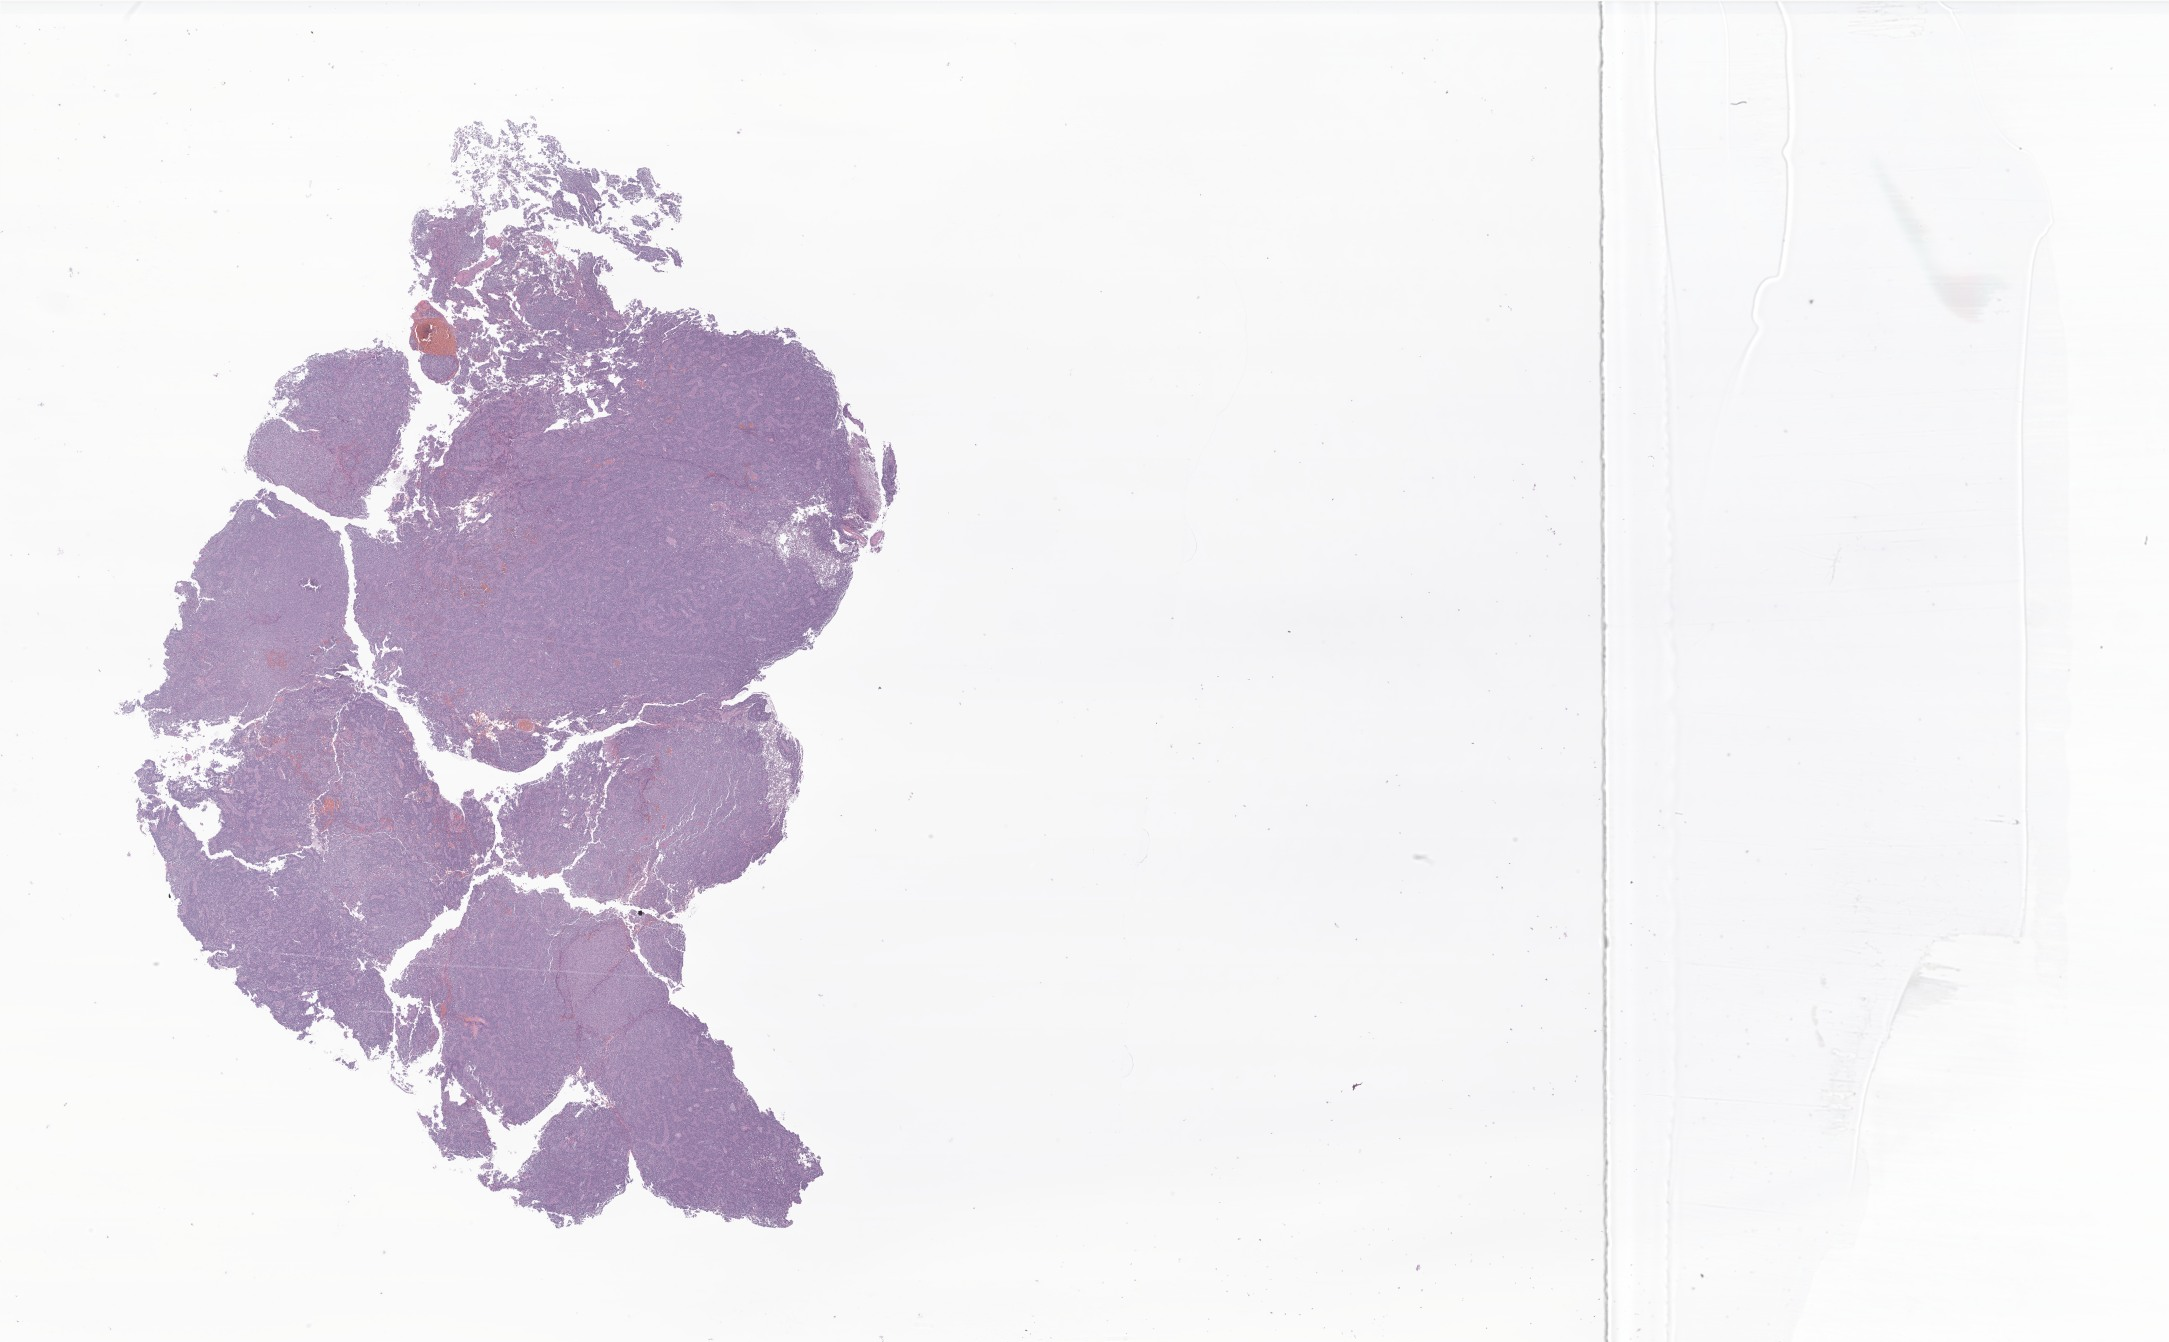
Haematoxylin and eosin whole-slide image of tumor tissue from the brain, low-resolution overview of the scanned area, about 36.6 x 22.6 mm, formalin-fixed, paraffin-embedded (FFPE) tissue. Patient: female, age 118 months.
Diagnosis: Glioma, malignant.